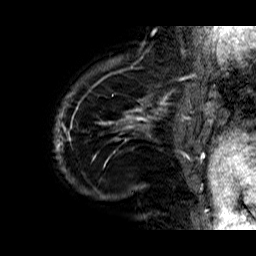
Breast MRI (dynamic contrast-enhanced), one sagittal slice. Position 5 of 60 along the scan axis. Dynamic contrast-enhanced series, time point 2 of 6 at this slice position (early post-contrast). 1.5 T. TE 6.3 ms, TR 32.9 ms. 4 mm slice thickness. 256 × 256 image matrix, field of view 200 × 200 mm. Female patient. Case-level facts recorded for this patient, not image findings: setting: breast cancer imaged before/during neoadjuvant chemotherapy; receptor status: HR-positive, HER2-negative.
Annotated regions visible in this slice (semi-automatic segmentation, software-assisted and operator-edited):
- analysis volume of interest (the breast-tissue region the enhancement analysis was run in; not a lesion): box from (x=54, y=74) to (x=176, y=204) px
- tumour enhancement mask (voxels above the 100 % enhancement threshold inside the analysis volume of interest): (x=54, y=82)–(x=172, y=198)